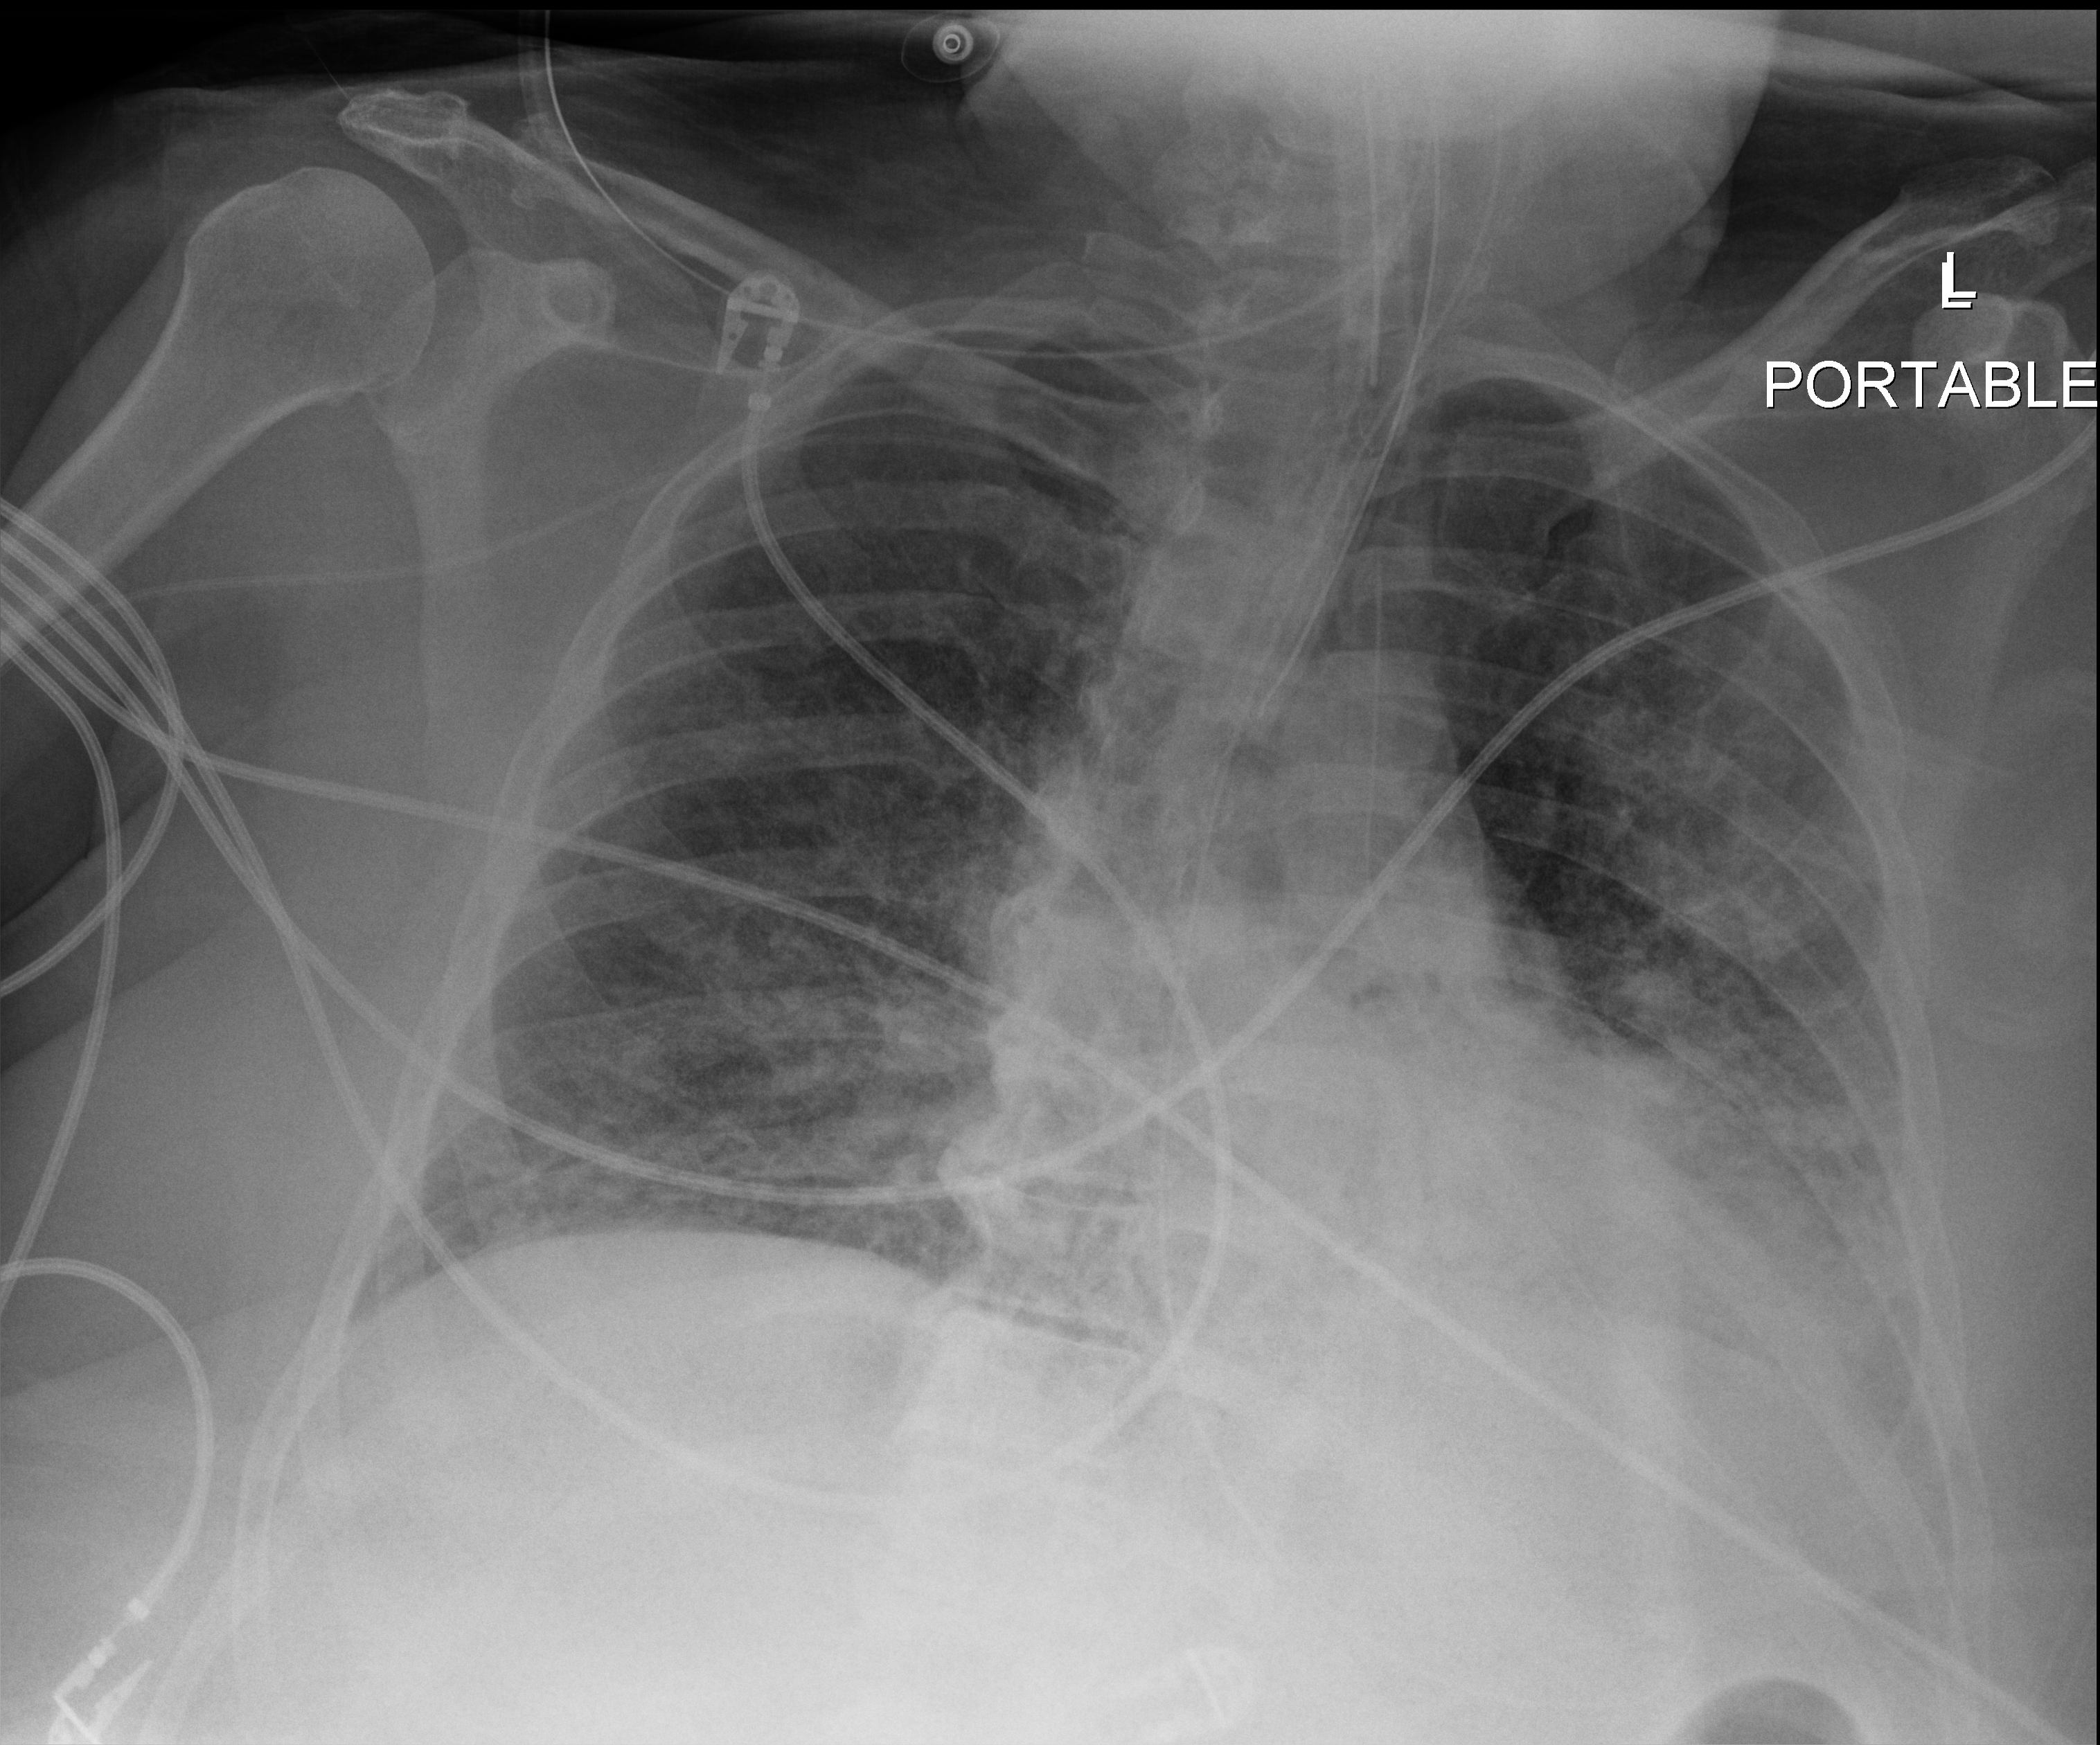
Chest X-ray; anteroposterior (AP) projection. Adult patient hospitalised with COVID-19, age 18–59 years.
Admission-level facts for this patient (not findings on this image; timing relative to this image not recorded): mechanically ventilated during this hospital stay: yes.